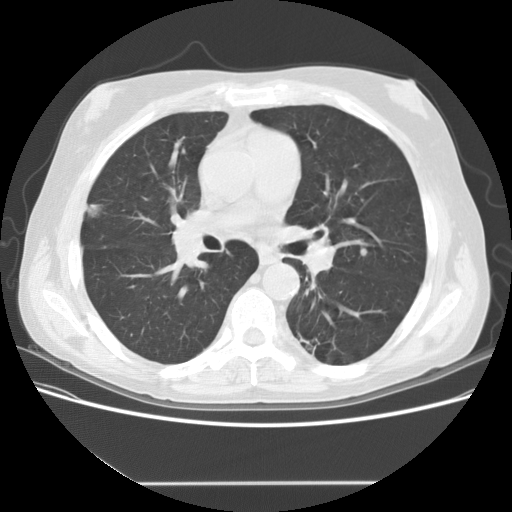
Low-dose screening chest CT, one axial slice; slice 89 of 153 in the series (ordered by position); reconstruction kernel STANDARD; lung window (W 1500 / L -600 HU); 2.5 mm slice thickness; 512 × 512 image matrix, field of view 360 × 360 mm.
Structures marked on this image (manually delineated by an expert):
- lesion 2 (tumor, upper lobe of right lung): bounding box (x1, y1, x2, y2) in pixels: (88, 204, 100, 217)